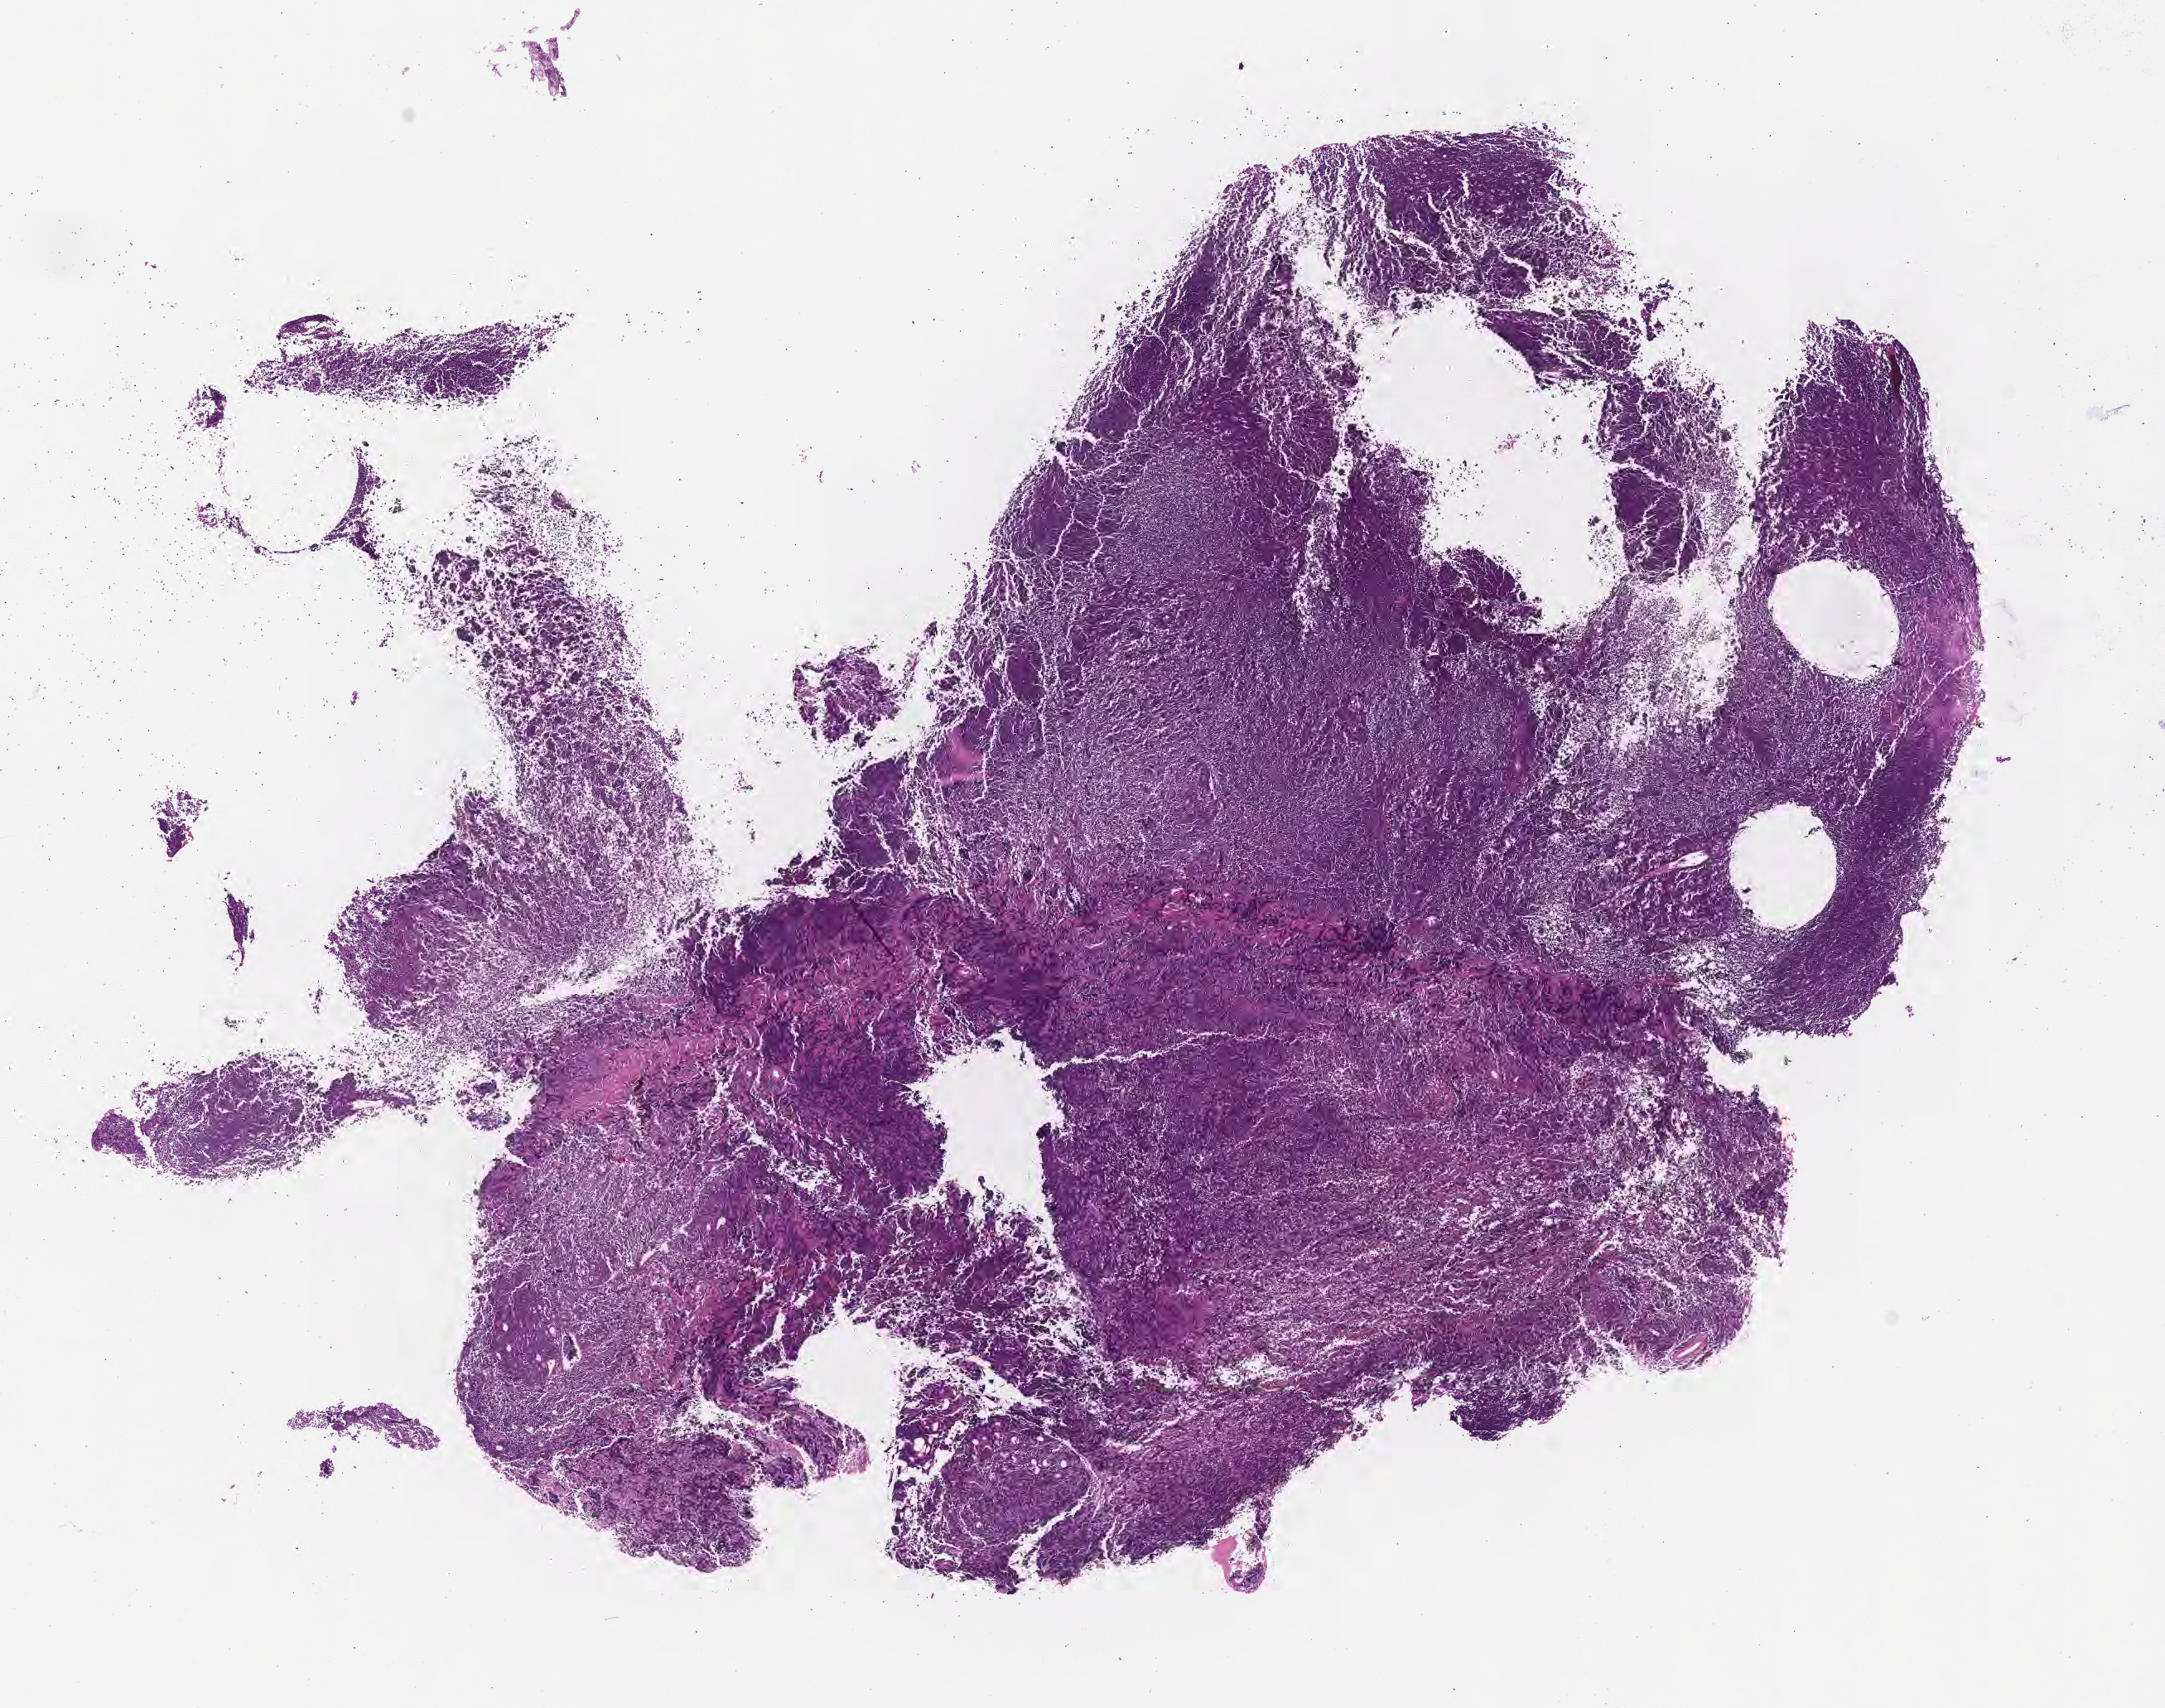
Whole-slide image, hematoxylin and eosin (H&E) stain, a low-resolution overview of the entire scanned area, about 10.6 x 8.3 mm, FFPE section, primary tumor. Male, age 3 years at initial diagnosis. Slide review estimates, as recorded: tumor cells 95%, tumor nuclei 95%, stromal cells 5%, necrosis 0%, normal cells 0%. Inflammatory infiltration, as recorded: lymphocyte infiltration 80%, monocyte infiltration 10%, neutrophil infiltration 0%.
Ann Arbor stage (patient): Stage IV. Diagnosis: Burkitt lymphoma, NOS. Section: top of the tissue portion.